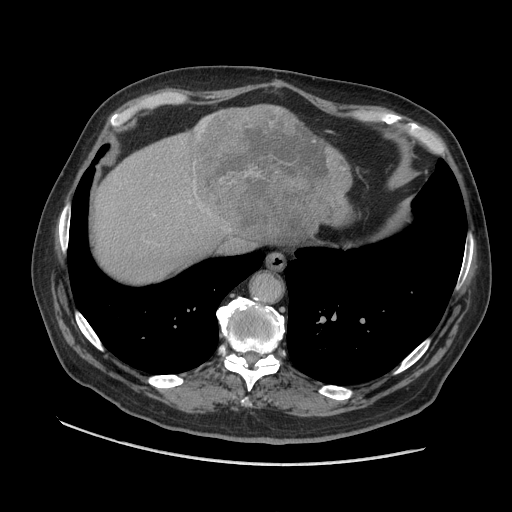
Contrast-enhanced abdominal CT (liver protocol), one axial slice. Position 85 of 109 along the scan axis. Reconstruction kernel STANDARD. 140 kVp. Soft-tissue window (W 400 / L 40 HU). 512 × 512 image matrix, field of view 420 × 420 mm. From the clinical record (not read from this slice): diagnosis: hepatocellular carcinoma (patient treated with transarterial chemoembolisation; whether this scan precedes or follows treatment is not stated here); TNM stage (as recorded): Stage-I; Child-Pugh class: A; tumour nodularity: uninodular.
Structures marked on this image (semi-automatically segmented with operator editing):
- liver parenchyma outside the tumour (the mass and vessels are separate outlines, so this box may not span the whole liver): bounding box <94,108,338,282> (left, top, right, bottom; pixels)
- mass: <191,103,352,242>